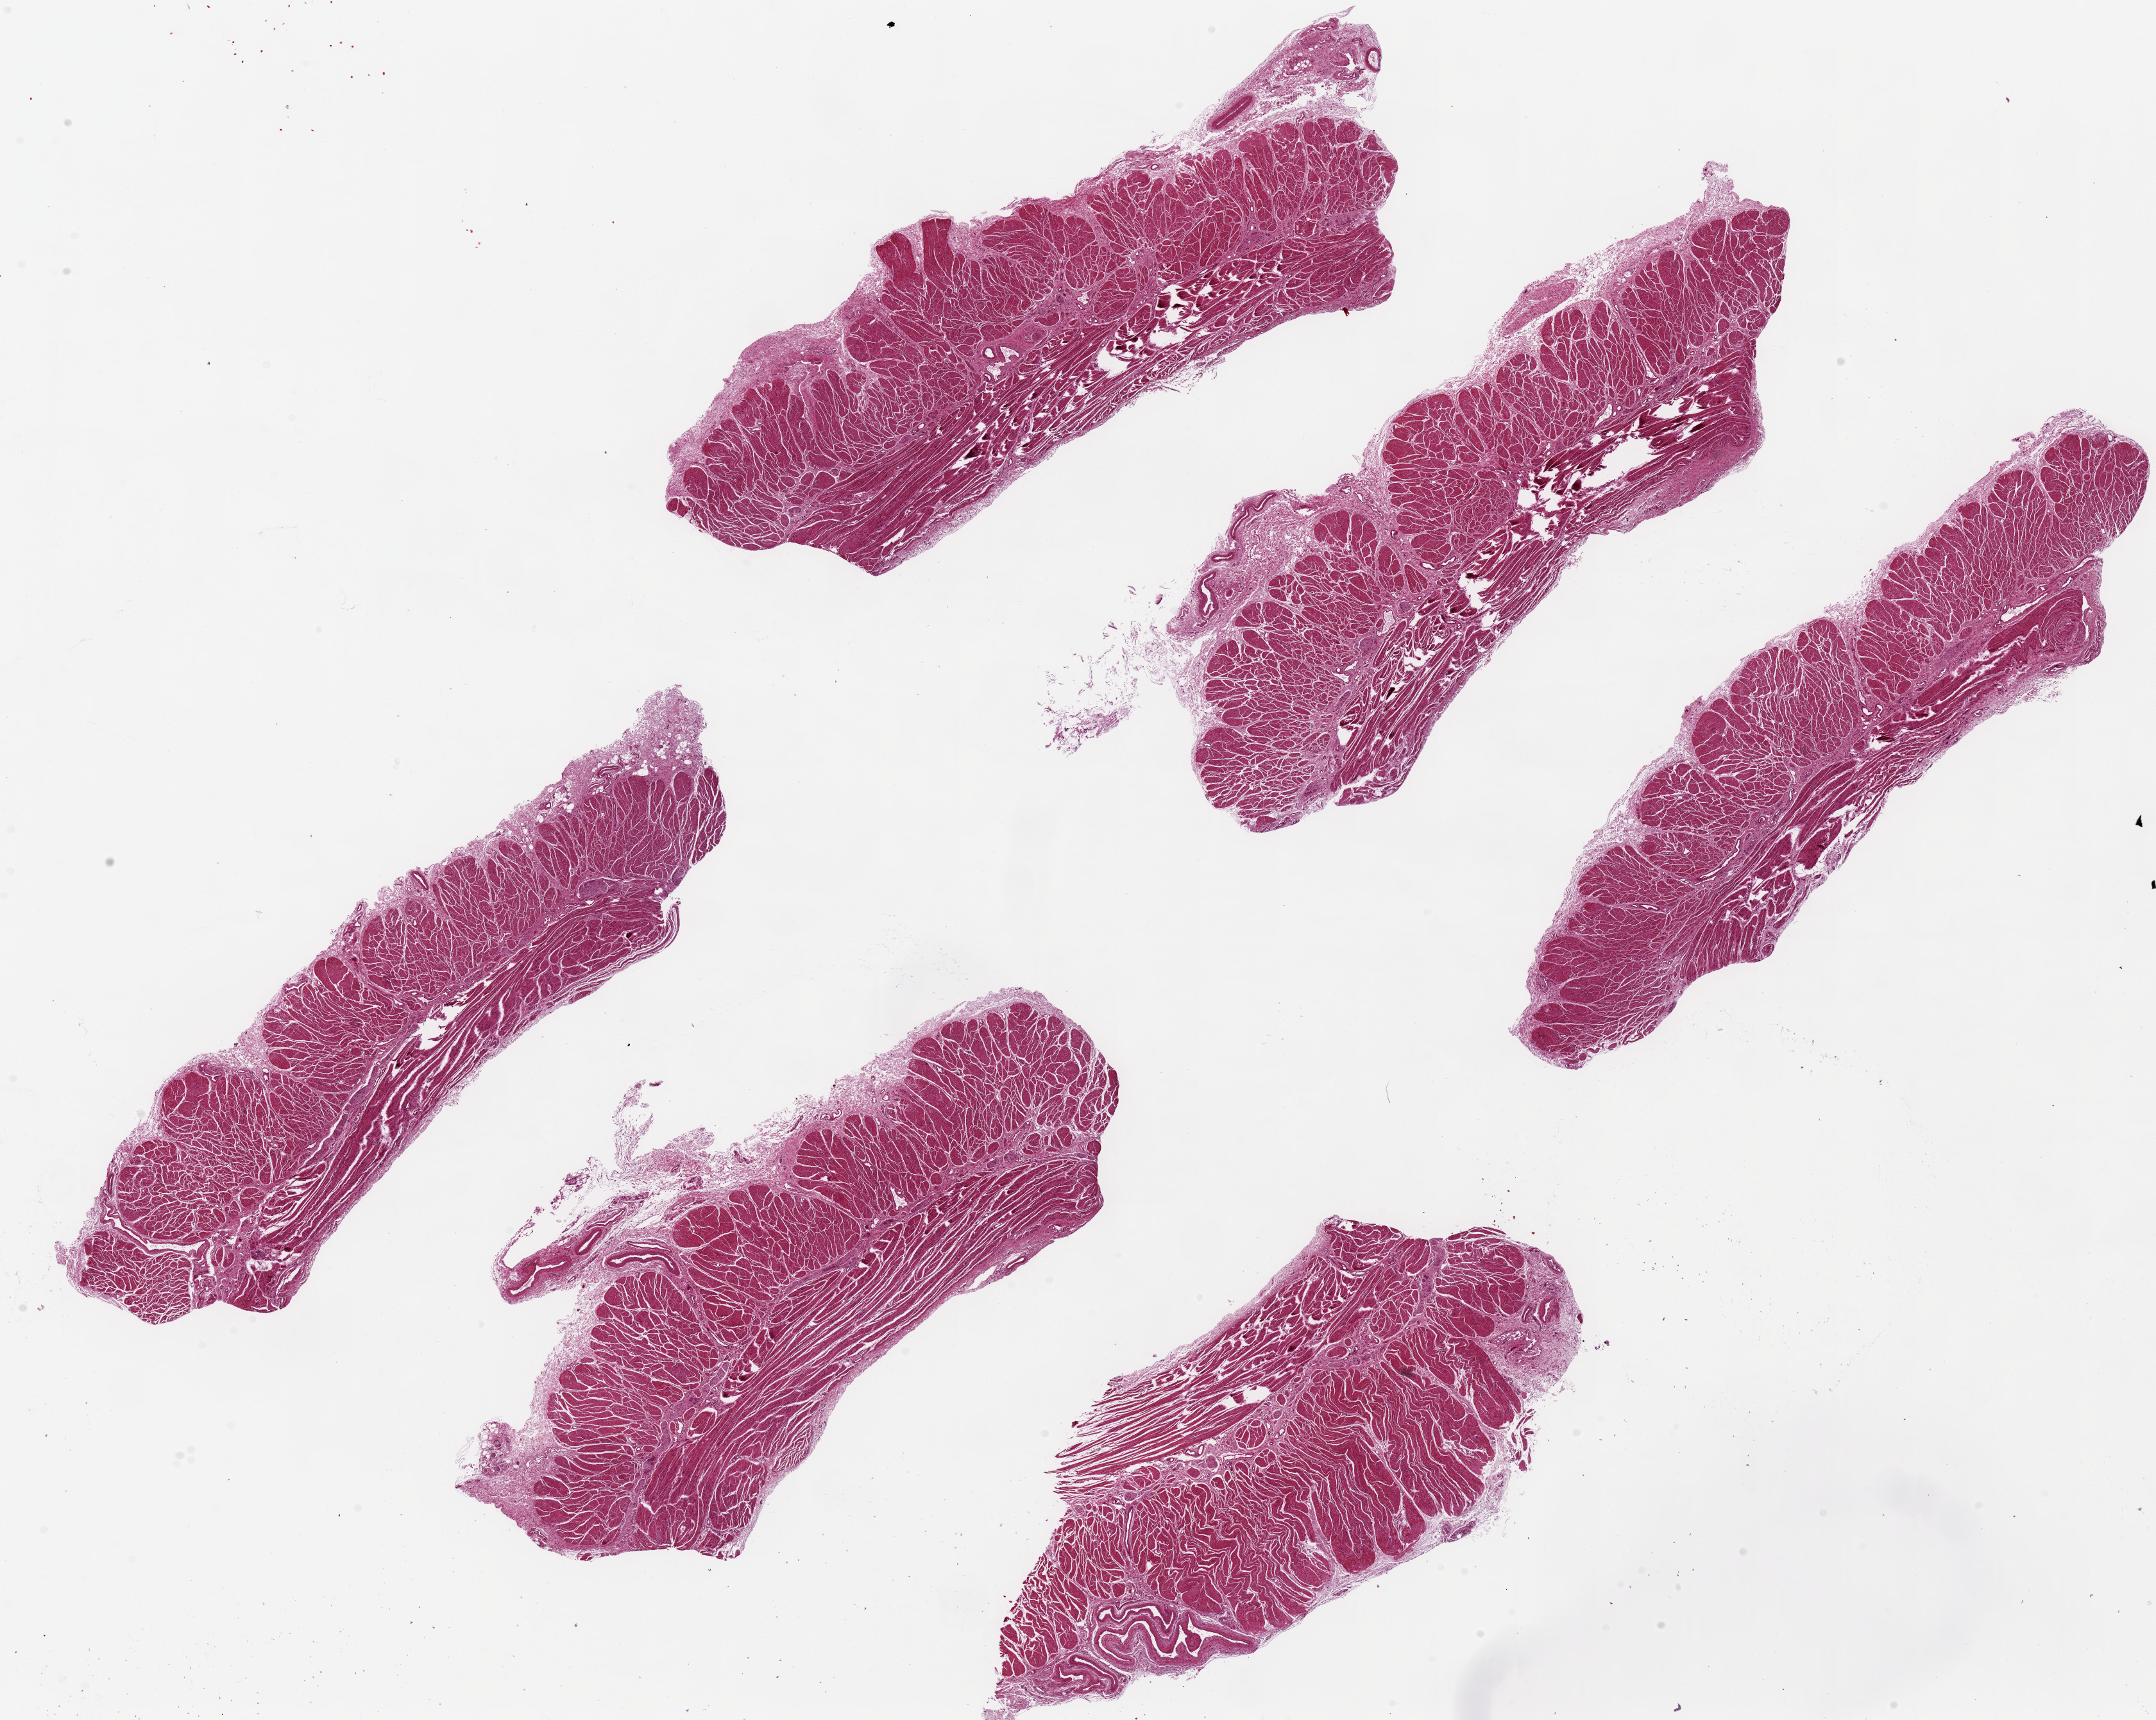
Hematoxylin and eosin (H&E) whole-slide image, brightfield — low-resolution overview of the scanned area, about 26.6 x 21.2 mm, PAXgene-fixed paraffin-embedded (PFPE) section, sampled site (target tissue): esophageal muscle, tissue donor sample. Donor: female.
Review note (as recorded): 6 ~9x3mm pieces.